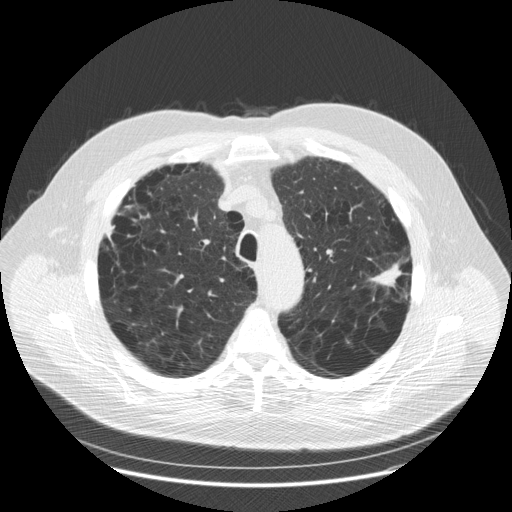
Axial slice from a low-dose chest CT screening exam. First (baseline) screen. Lung window (W 1500 / L -600 HU). 2.5 mm slice thickness. 512 × 512 image matrix. Male, age 70 years at enrolment. Current smoker at enrolment.
- Lesion marked by an expert reader, bounding box [x1, y1, x2, y2] px = [362, 248, 417, 299].
- Reader record for this screening exam (exam-level; its link to the box is not recorded): non-calcified nodule or mass ≥4 mm, left upper lobe, 25 × 13 mm, spiculated (stellate) margins, soft tissue attenuation.
- Lung cancer was diagnosed 62 days after this screen: adenocarcinoma, NOS, left upper lobe, moderately differentiated (G2), stage IA (AJCC 6th edition), 22 mm at pathology.